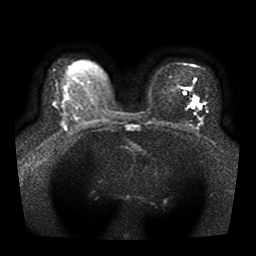
Breast MRI, one axial slice. Position 23 of 41 along the scan axis. Diffusion-weighted series; image 2 of 4 stored at this slice position (different b-values; order by instance number). 1.5 T. 5 mm slice thickness. 256 × 256 image matrix, field of view 330 × 330 mm. Female patient.
Structures marked on this image (manually delineated by an expert):
- tumour on diffusion-weighted imaging: bounding box [x1, y1, x2, y2] px = [192, 105, 195, 108]